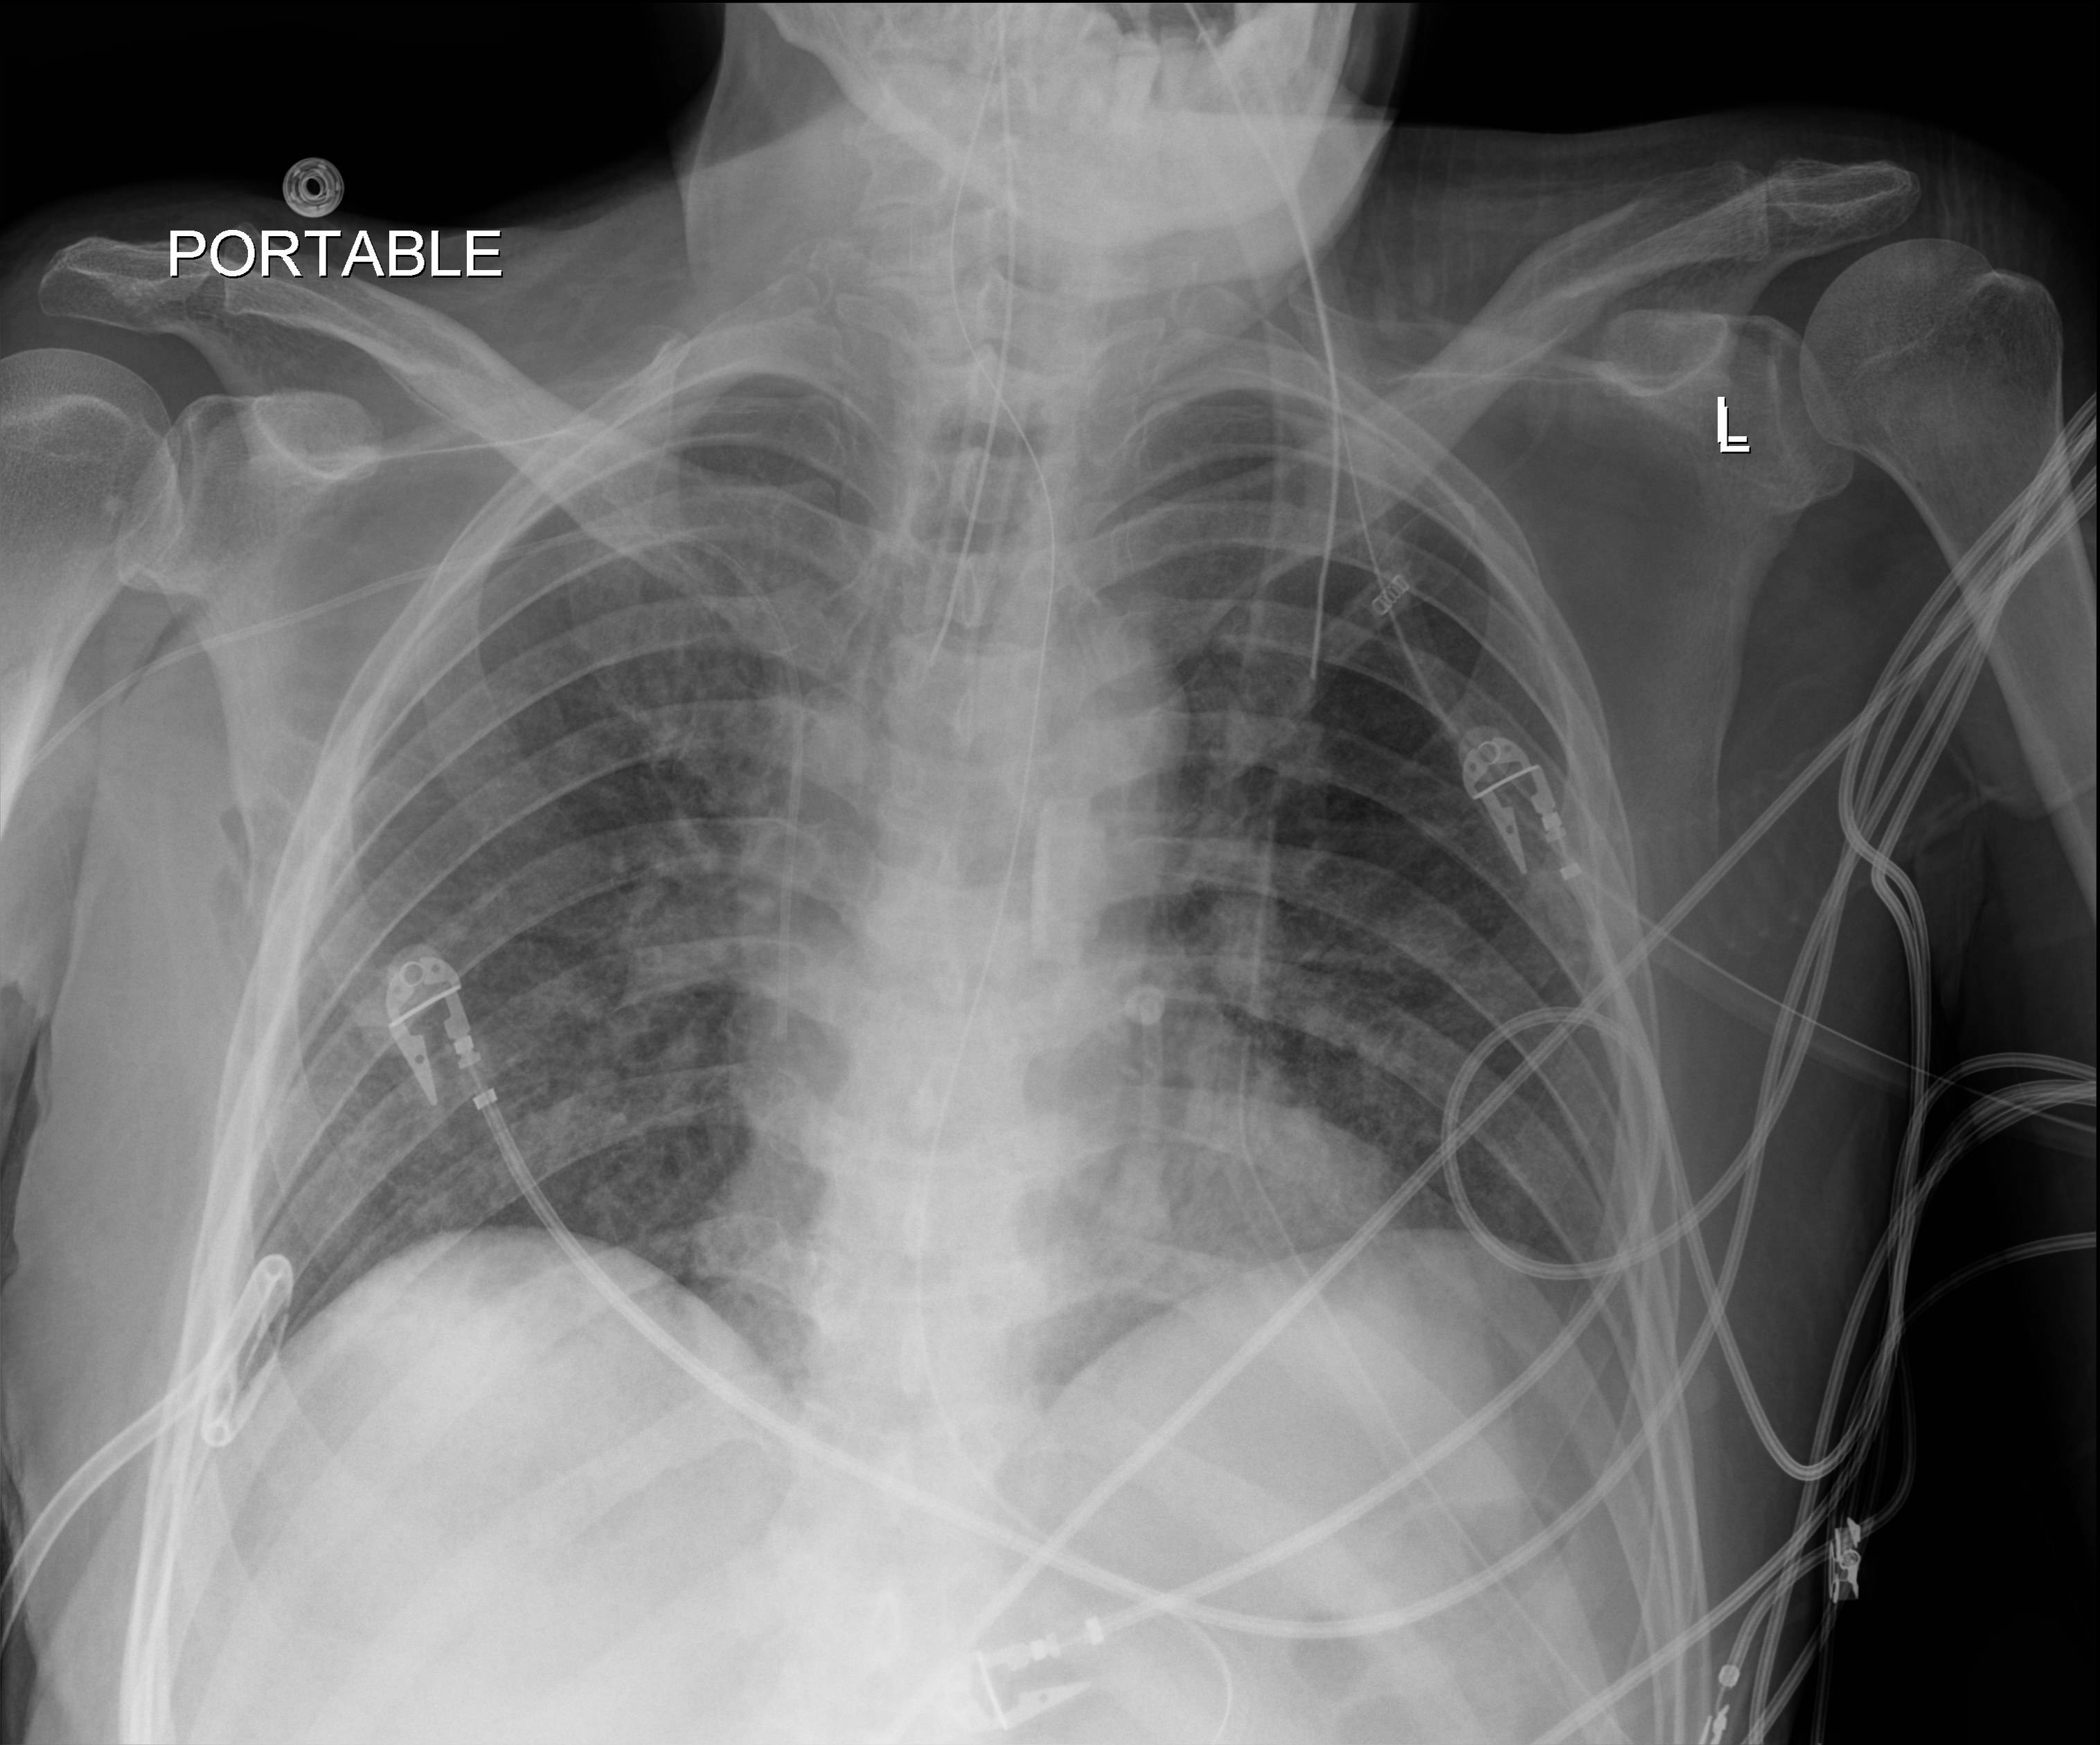
Portable chest radiograph, anteroposterior (AP) projection. Male patient hospitalised with COVID-19, age 18–59 years.
Hospital-stay facts (about this admission, not read from this image; timing relative to this image not recorded):
- diabetes (admission record): no
- hypertension (admission record): no
- admitted to intensive care during this hospital stay: yes